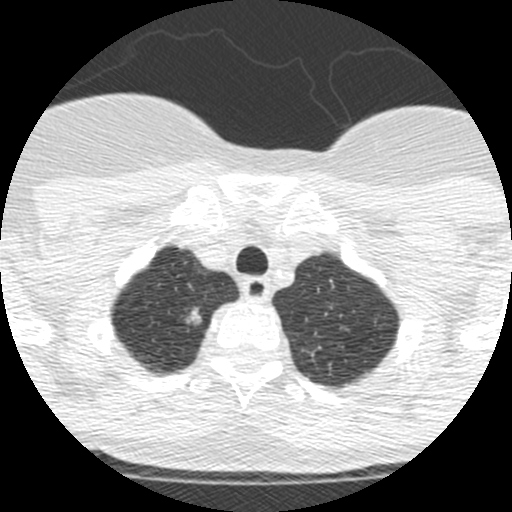
Low-dose screening chest CT, one axial slice. Slice 216 of 250 in the series (ordered by position). Reconstruction kernel STANDARD. Lung window (W 1500 / L -600 HU). 1.25 mm slice thickness. 512 × 512 image matrix.
Annotated regions visible in this slice (expert manual segmentation):
- lesion 1 (tumor, upper lobe of right lung): box from (x=186, y=307) to (x=202, y=325) px